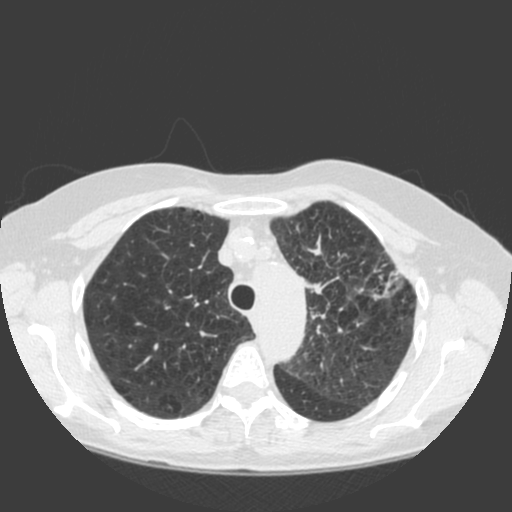
Low-dose screening chest CT, one axial slice. Position 146 of 184 along the scan axis. 120 kVp. Lung window (W 1500 / L -600 HU). 2 mm slice thickness. 512 × 512 image matrix, field of view 350 × 350 mm.
Outlined on this slice (outlined manually by an expert reader):
- lesion 1 (tumor, hilum of left lung): bounding box (x1, y1, x2, y2) in pixels: (309, 283, 326, 294)